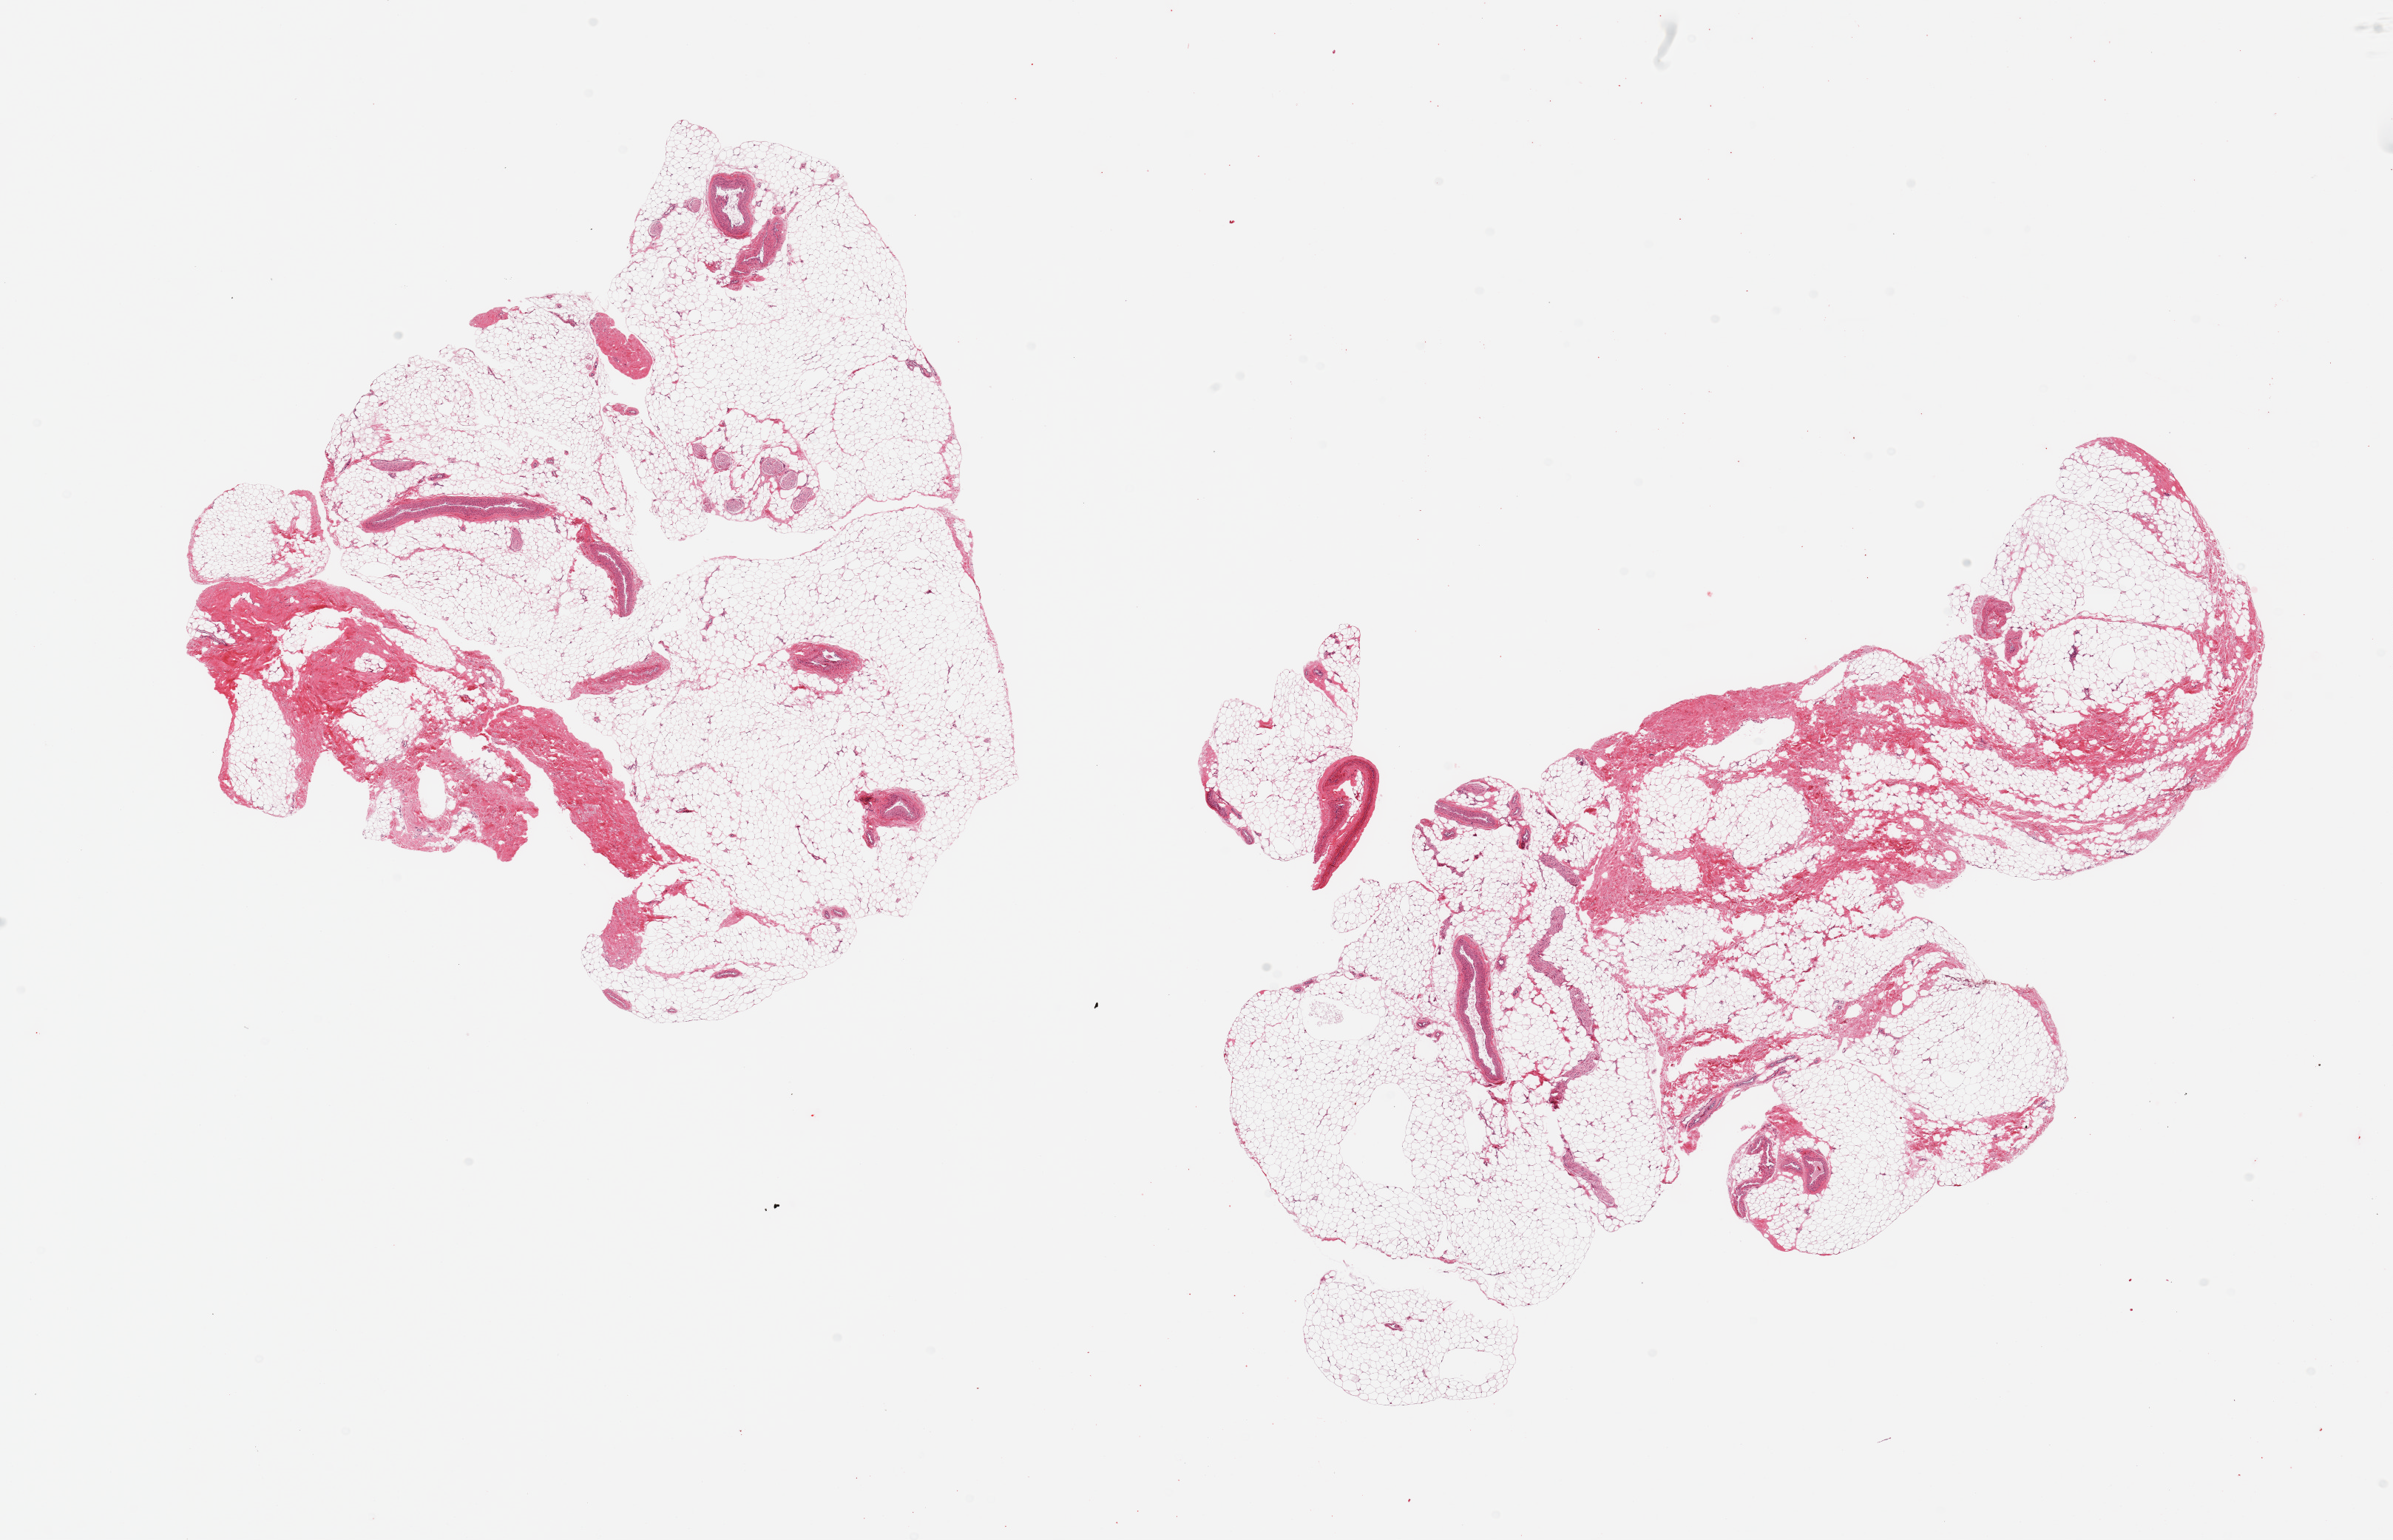
Digitized haematoxylin and eosin-stained section — a low-resolution overview of the entire scanned area, about 25.6 x 16.5 mm (acquisition: 20x scan), PAXgene-fixed, paraffin-embedded tissue, section of breast (target tissue), donor tissue sample.
- pathologist's review note for this sample: 2 pieces; fat and fibrocollagenous tissue with several large vessels and nerve, no ducts seen